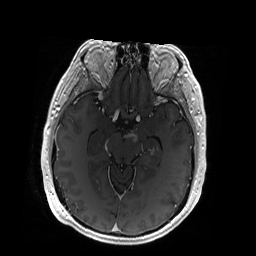
Brain MRI from a brain-tumour surgery series, one axial slice; position 113 of 192 along the scan axis; T1-weighted post-contrast; 1 mm slice thickness; 256 × 256 image matrix, field of view 256 × 256 mm. From the clinical record (not read from this slice): histopathology: Glioblastoma; WHO grade: 4; IDH mutation: no.
Outlined on this slice (outlined manually by an expert reader):
- tumour: bounding box <127,132,159,154> (left, top, right, bottom; pixels)